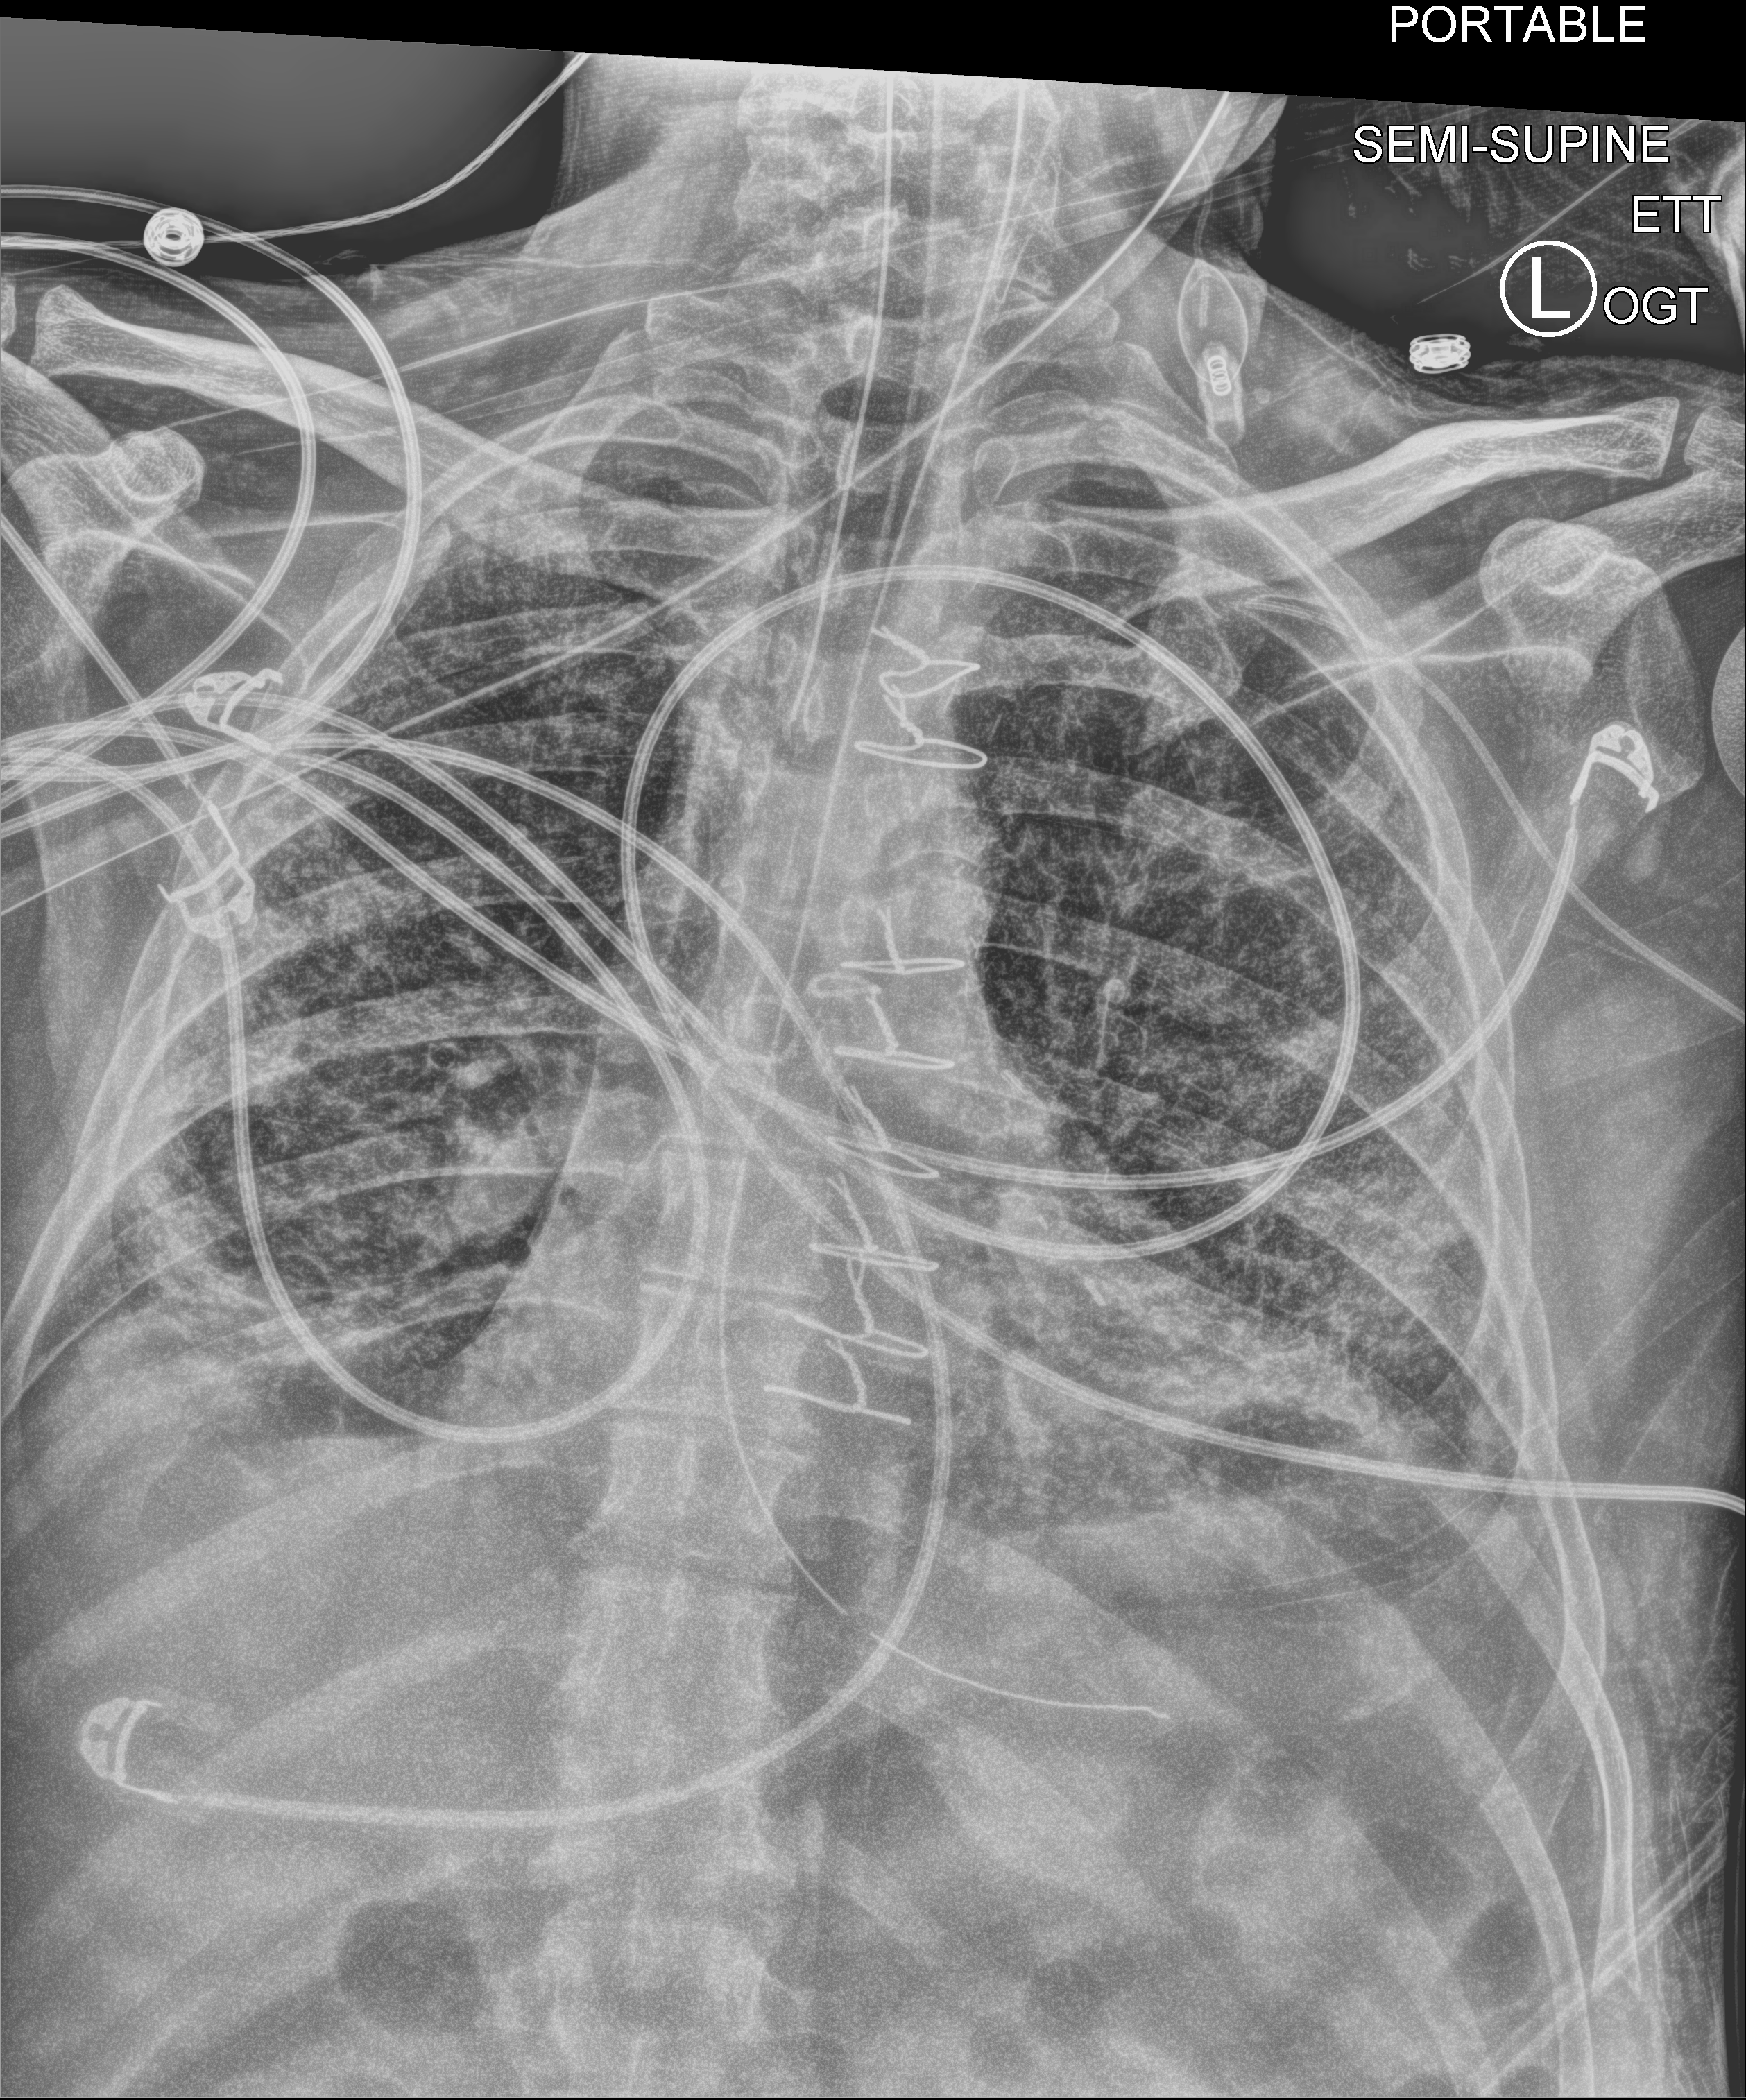
Bedside chest radiograph (computed radiography), anteroposterior (AP) projection. Patient hospitalised with COVID-19; male, aged 18–59 years.
Hospital-stay facts (about this admission, not read from this image; timing relative to this image not recorded): admitted to intensive care during this hospital stay: yes.